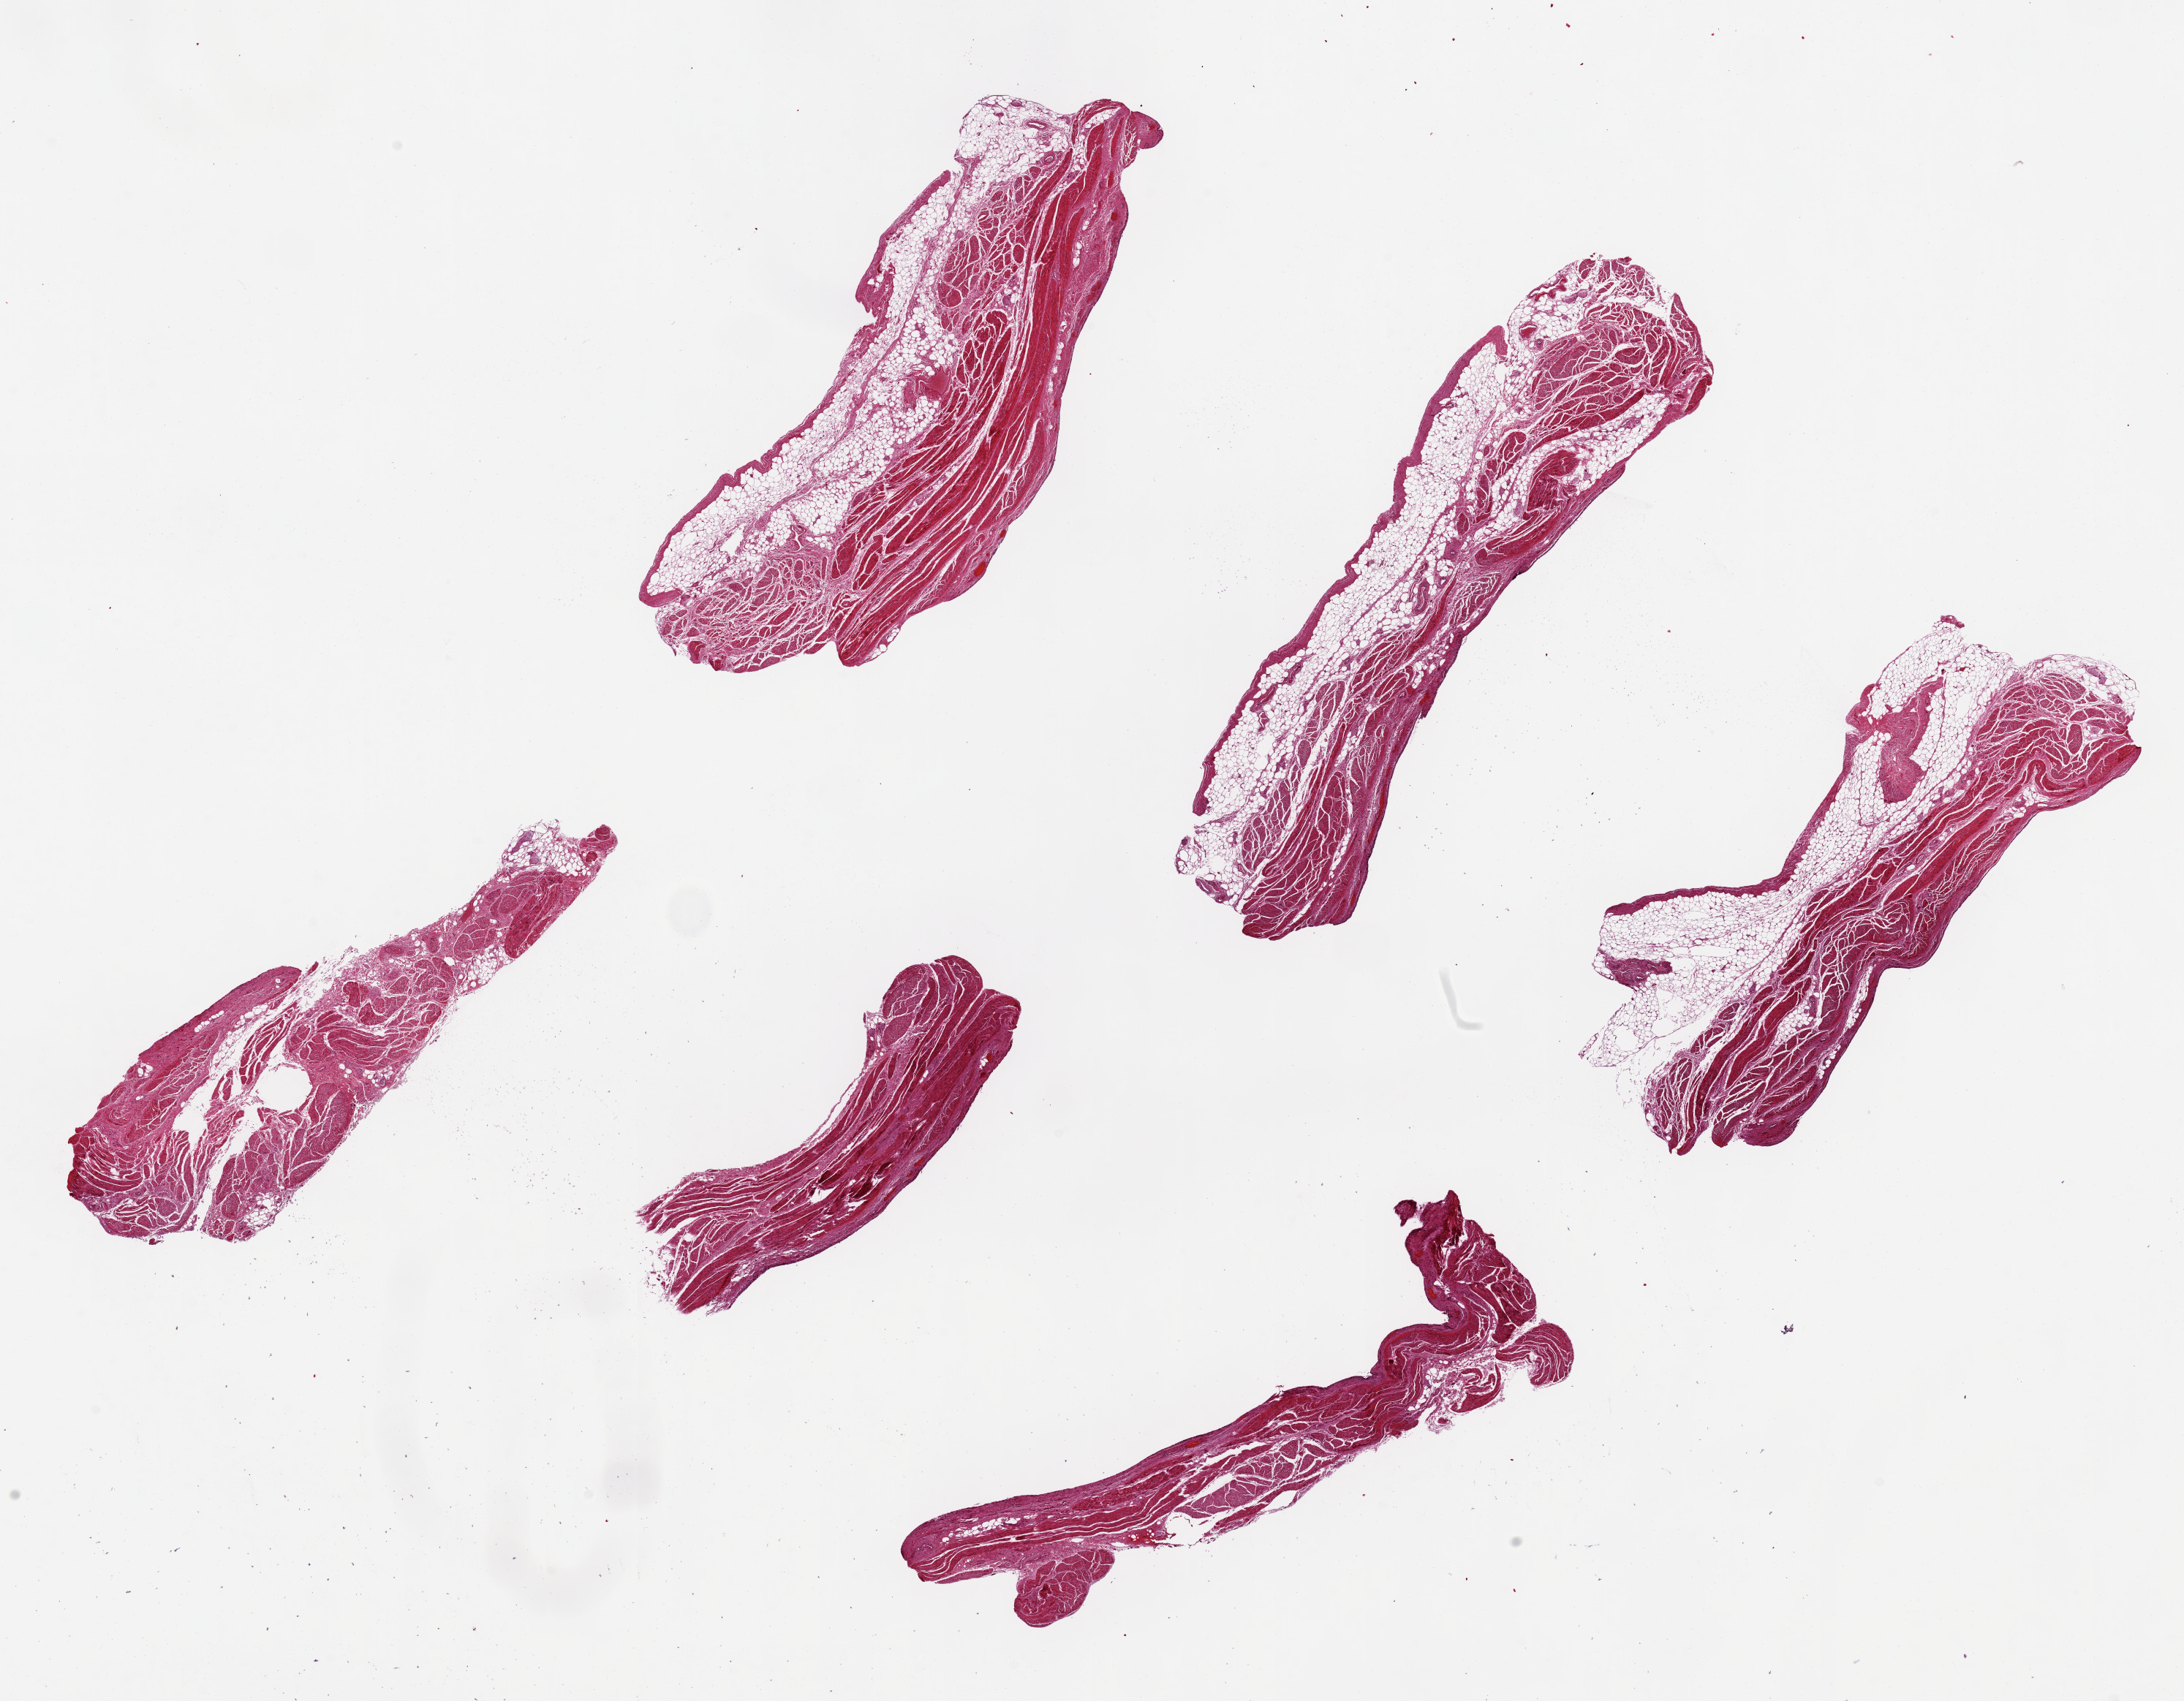
Haematoxylin and eosin whole-slide image, a low-resolution overview of the entire scanned area, about 23.6 x 18.4 mm (acquisition: 20x scan). PAXgene-fixed paraffin-embedded (PFPE) section. Sampled site (target tissue): urinary bladder. Tissue donor sample. Female donor.
* reviewer comment on this tissue sample: 6 pieces up to 8x2.5 mm; epithelium totally sloughed